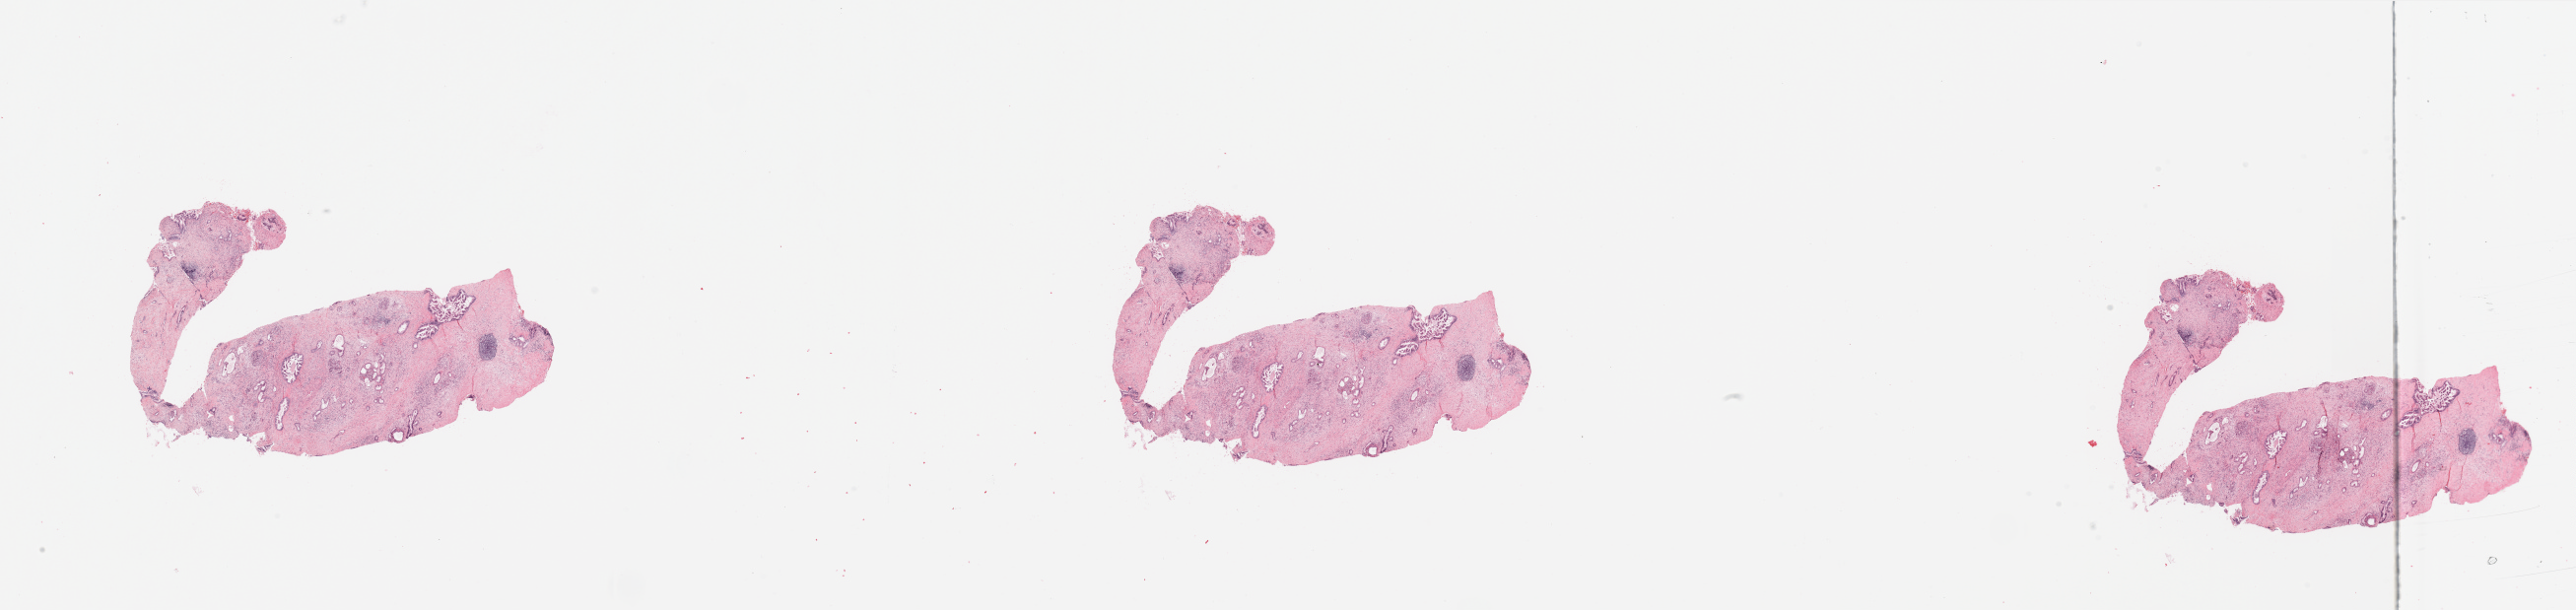
Whole-slide histology image, Hematoxylin and eosin (H&E) stained — shown as a low-resolution overview of the whole scanned area (about 41.3 x 9.8 mm, from a 20x scan); tumour tissue sample, sampled site: pancreas. Patient: male, age 71 years. Histologic grade: G2 (moderately differentiated). Composition of this section per pathologist review: tumour nuclei 20%, necrosis 1%.
Primary tumour site (as recorded): body. Diagnosis: Infiltrating duct carcinoma, NOS. AJCC pathologic stage: IIB.